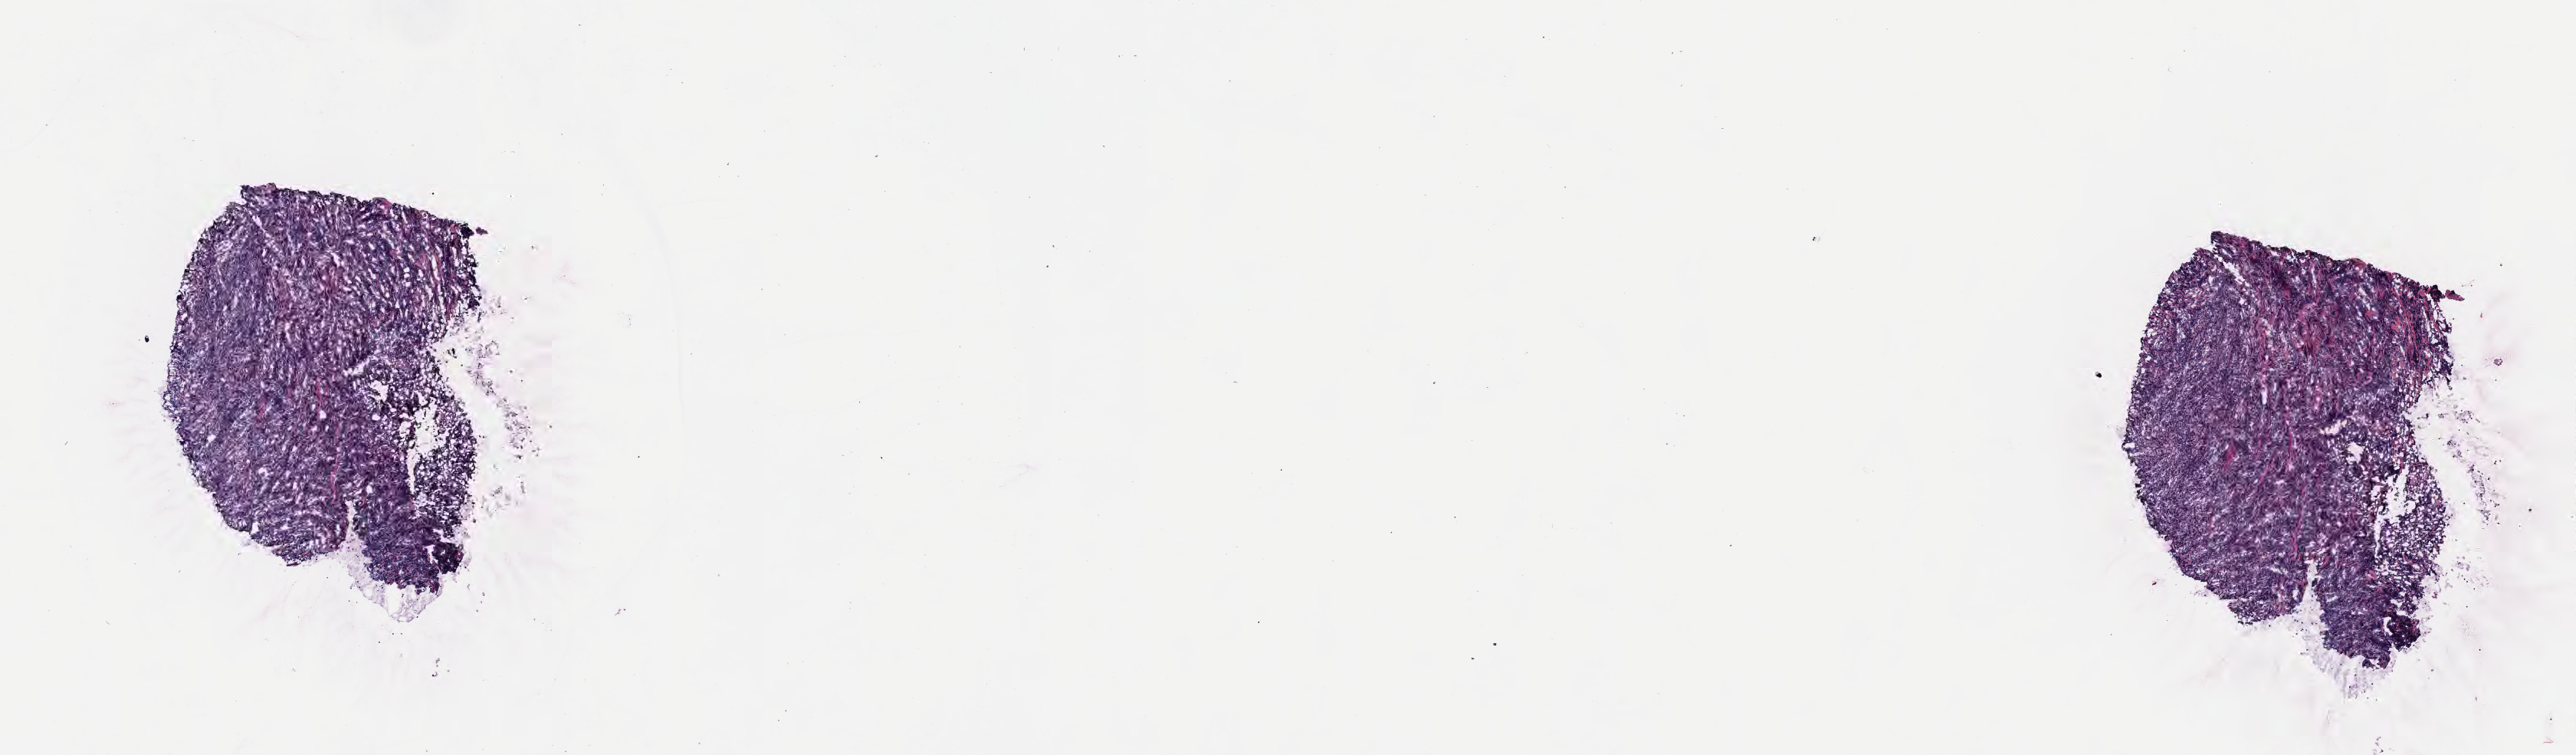
Whole-slide image, haematoxylin and eosin stain — whole scanned area (about 13.6 x 4.0 mm) shown as a low-resolution overview. Frozen section. Specimen: primary tumor. Anatomic site: buccal mucosa. Male patient; age at initial diagnosis 7 years. Pathologist review of this section (percent, as recorded): tumor cells 95%, tumor nuclei 95%, stromal cells 3%, necrosis 2%, normal cells 0%. Inflammatory infiltration, as recorded: lymphocyte infiltration 60%, monocyte infiltration 20%, neutrophil infiltration 0%.
* histologic diagnosis: Burkitt lymphoma, NOS
* Ann Arbor stage (patient): Stage I
* section: top of the tissue portion